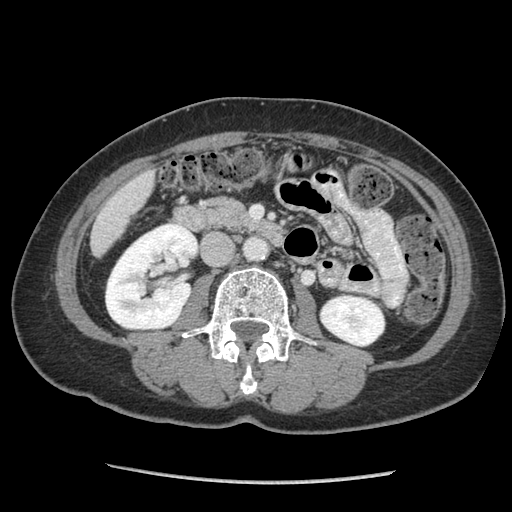
Contrast-enhanced abdominal CT (liver protocol), one axial slice; slice 19 of 105 in the series (ordered by position); reconstruction kernel STANDARD; soft-tissue window (W 400 / L 40 HU); 2.5 mm slice thickness; 512 × 512 image matrix, field of view 340 × 340 mm. Case-level facts recorded for this patient, not image findings: diagnosis: hepatocellular carcinoma (patient treated with transarterial chemoembolisation; whether this scan precedes or follows treatment is not stated here); TNM stage (as recorded): Stage-I; Child-Pugh class: A; tumour differentiation: moderately differentiated; tumour size: 11.1 cm.
Structures marked on this image (semi-automatic segmentation, software-assisted and operator-edited):
- liver parenchyma outside the tumour (the mass and vessels are separate outlines, so this box may not span the whole liver): bounding box [x1, y1, x2, y2] px = [90, 170, 154, 255]